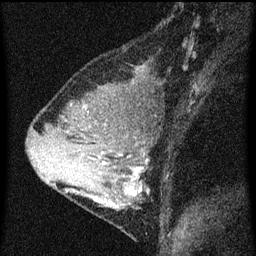
Breast MRI (dynamic contrast-enhanced), one sagittal slice. Slice 27 of 60 in the series (ordered by position). Dynamic contrast-enhanced series, image 2 of 3 at this slice position (ordered by acquisition). 1.5 T. TE 4.2 ms, TR 8 ms. 256 × 256 image matrix, field of view 180 × 180 mm. Female patient, age 33 years.
Outlined on this slice (semi-automatic segmentation, software-assisted and operator-edited):
- analysis volume of interest (the breast-tissue region the enhancement analysis was run in; not a lesion): box from (x=67, y=118) to (x=161, y=215) px
- tumour enhancement mask (voxels above the 70 % enhancement threshold inside the analysis volume of interest): (x=92, y=154)–(x=149, y=203)